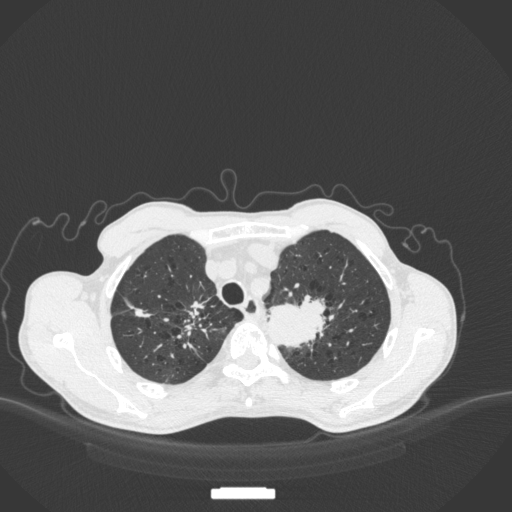
Chest CT, one axial slice; position 350 of 394 along the scan axis; reconstruction kernel B31f; 120 kVp; lung window (W 1500 / L -600 HU); 1 mm slice thickness; 512 × 512 image matrix, field of view 400 × 400 mm. Patient: male, 65 years. From the clinical record (not read from this slice): clinical TNM (as recorded): T2b N0 M0.
Structures marked on this image (rectangle marked by the reading radiologist):
- lung tumour (recorded histology: adenocarcinoma): bounding box (x1, y1, x2, y2) in pixels: (262, 289, 329, 350)